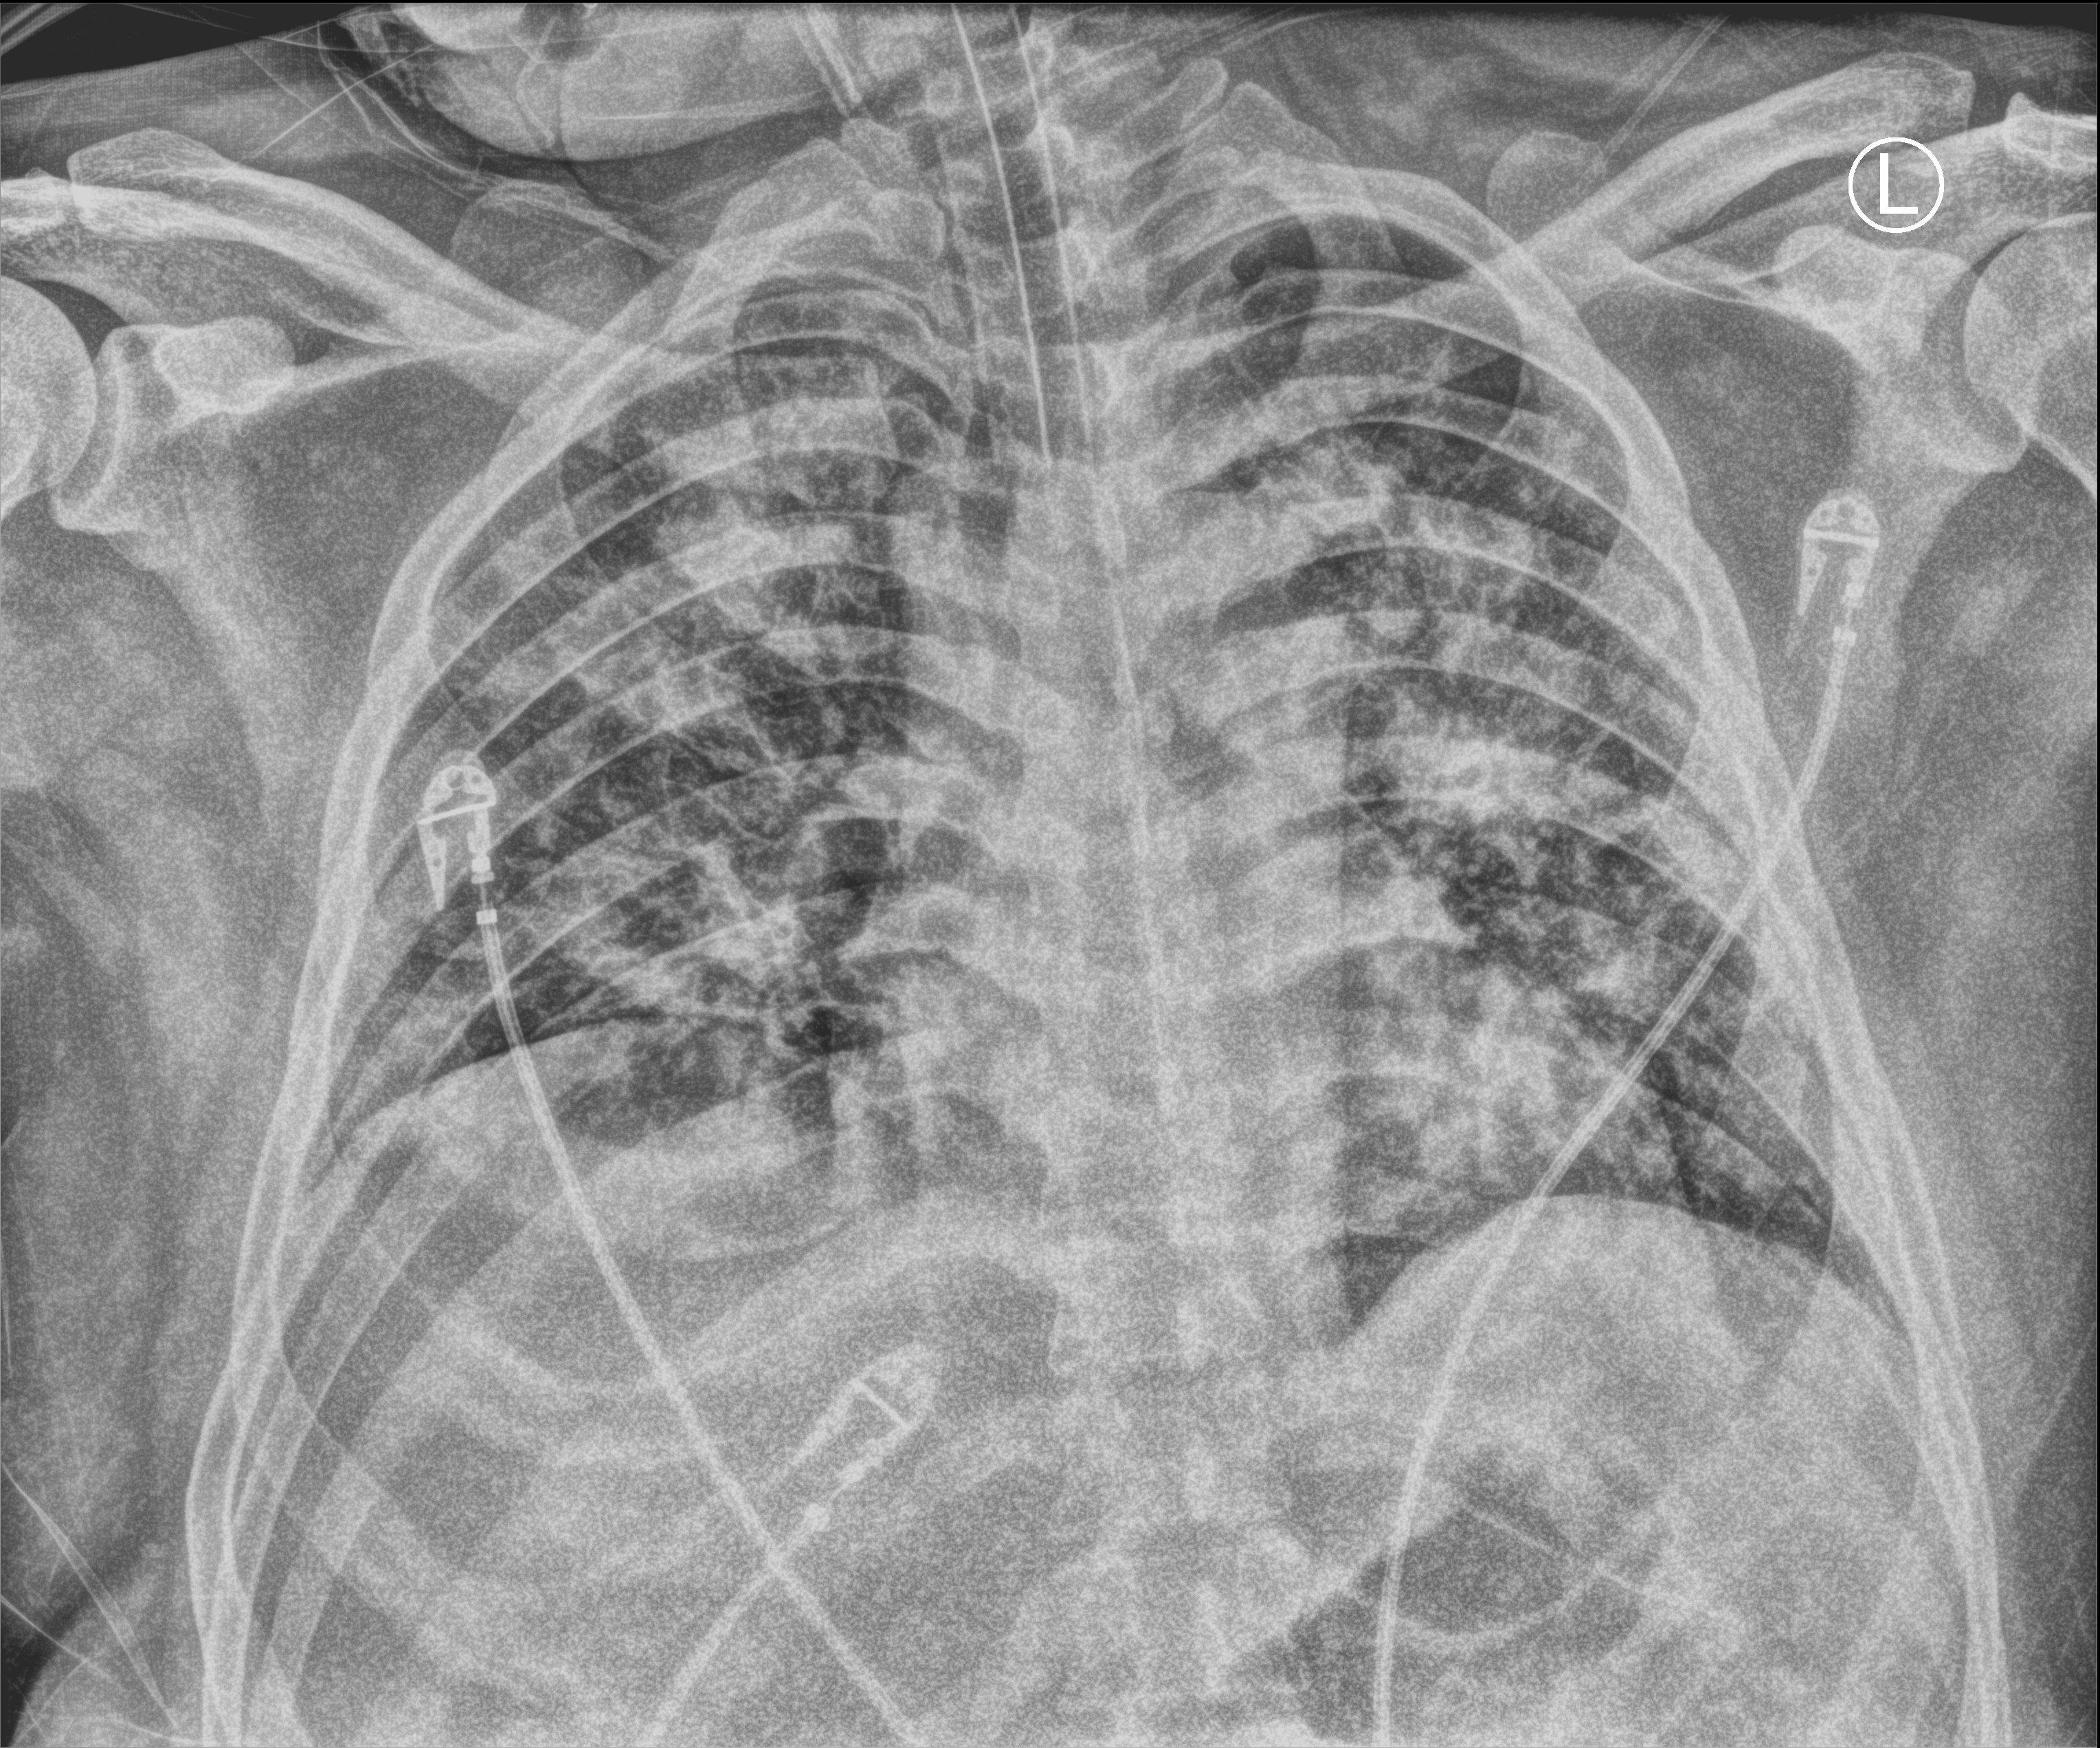
Bedside chest radiograph (computed radiography). Patient hospitalised with COVID-19; male, aged 18–59 years.
Hospital-stay facts (about this admission, not read from this image; timing relative to this image not recorded): length of hospital stay: 29 days; mechanically ventilated during this hospital stay: yes.